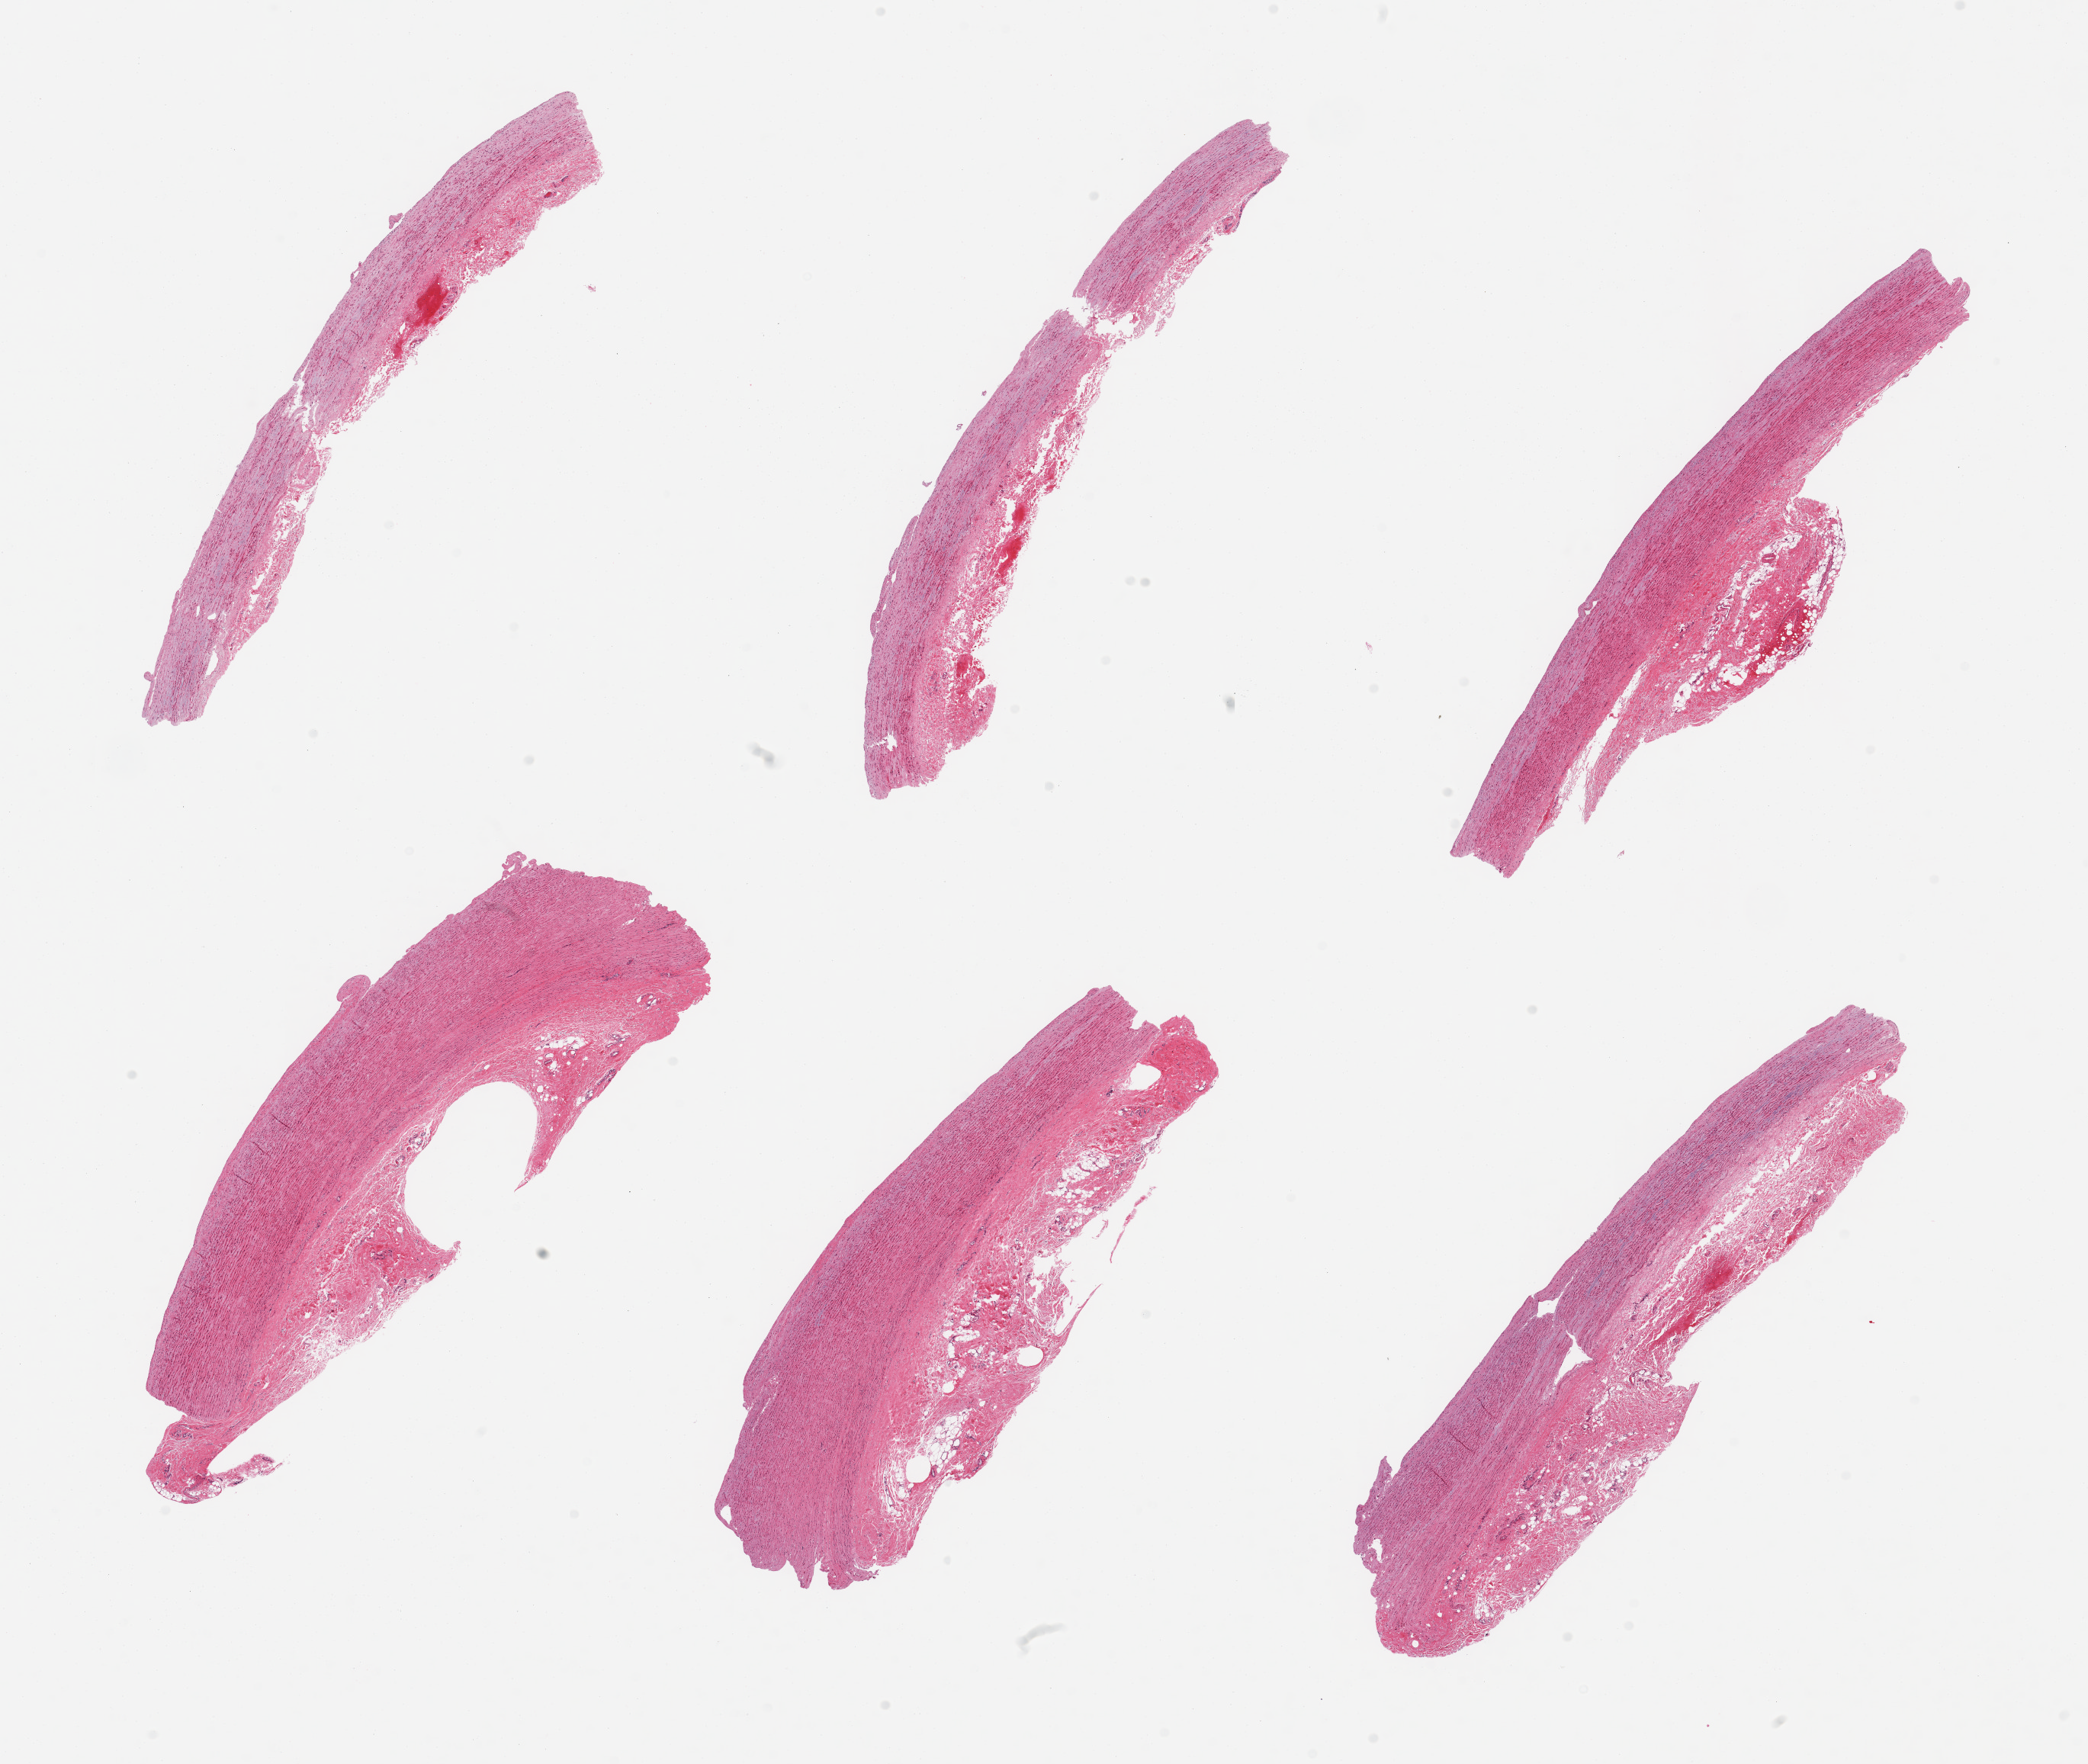
Whole-slide image, hematoxylin and eosin (H&E) stain, low-resolution overview of the scanned area, about 21.7 x 18.3 mm, PAXgene-fixed, paraffin-embedded tissue, target tissue: aorta, donor tissue sample. Donor: male.
- review note (as recorded): 6 pieces, adherent serosa/fat up to ~1mm